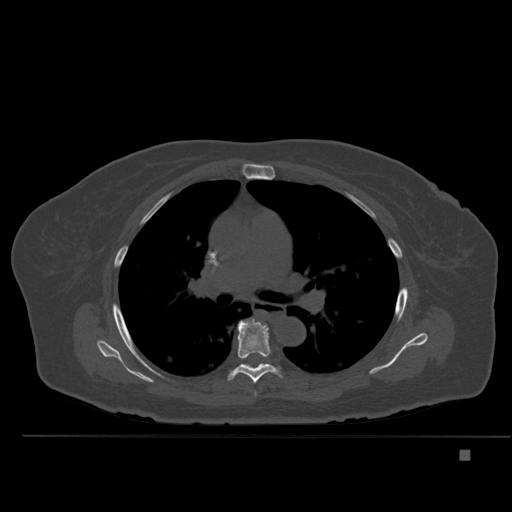
CT including the spine, one axial slice. Position 339 of 477 along the scan axis. Bone window (W 1800 / L 400 HU). 512 × 512 image matrix. Female patient, age 74 years. From the clinical record (not read from this slice): primary cancer: colon.
Annotated regions visible in this slice (semi-automatically segmented with operator editing):
- T6 vertebra: bounding box <228,318,281,384> (left, top, right, bottom; pixels)
- T7 vertebra: <260,364,266,366>